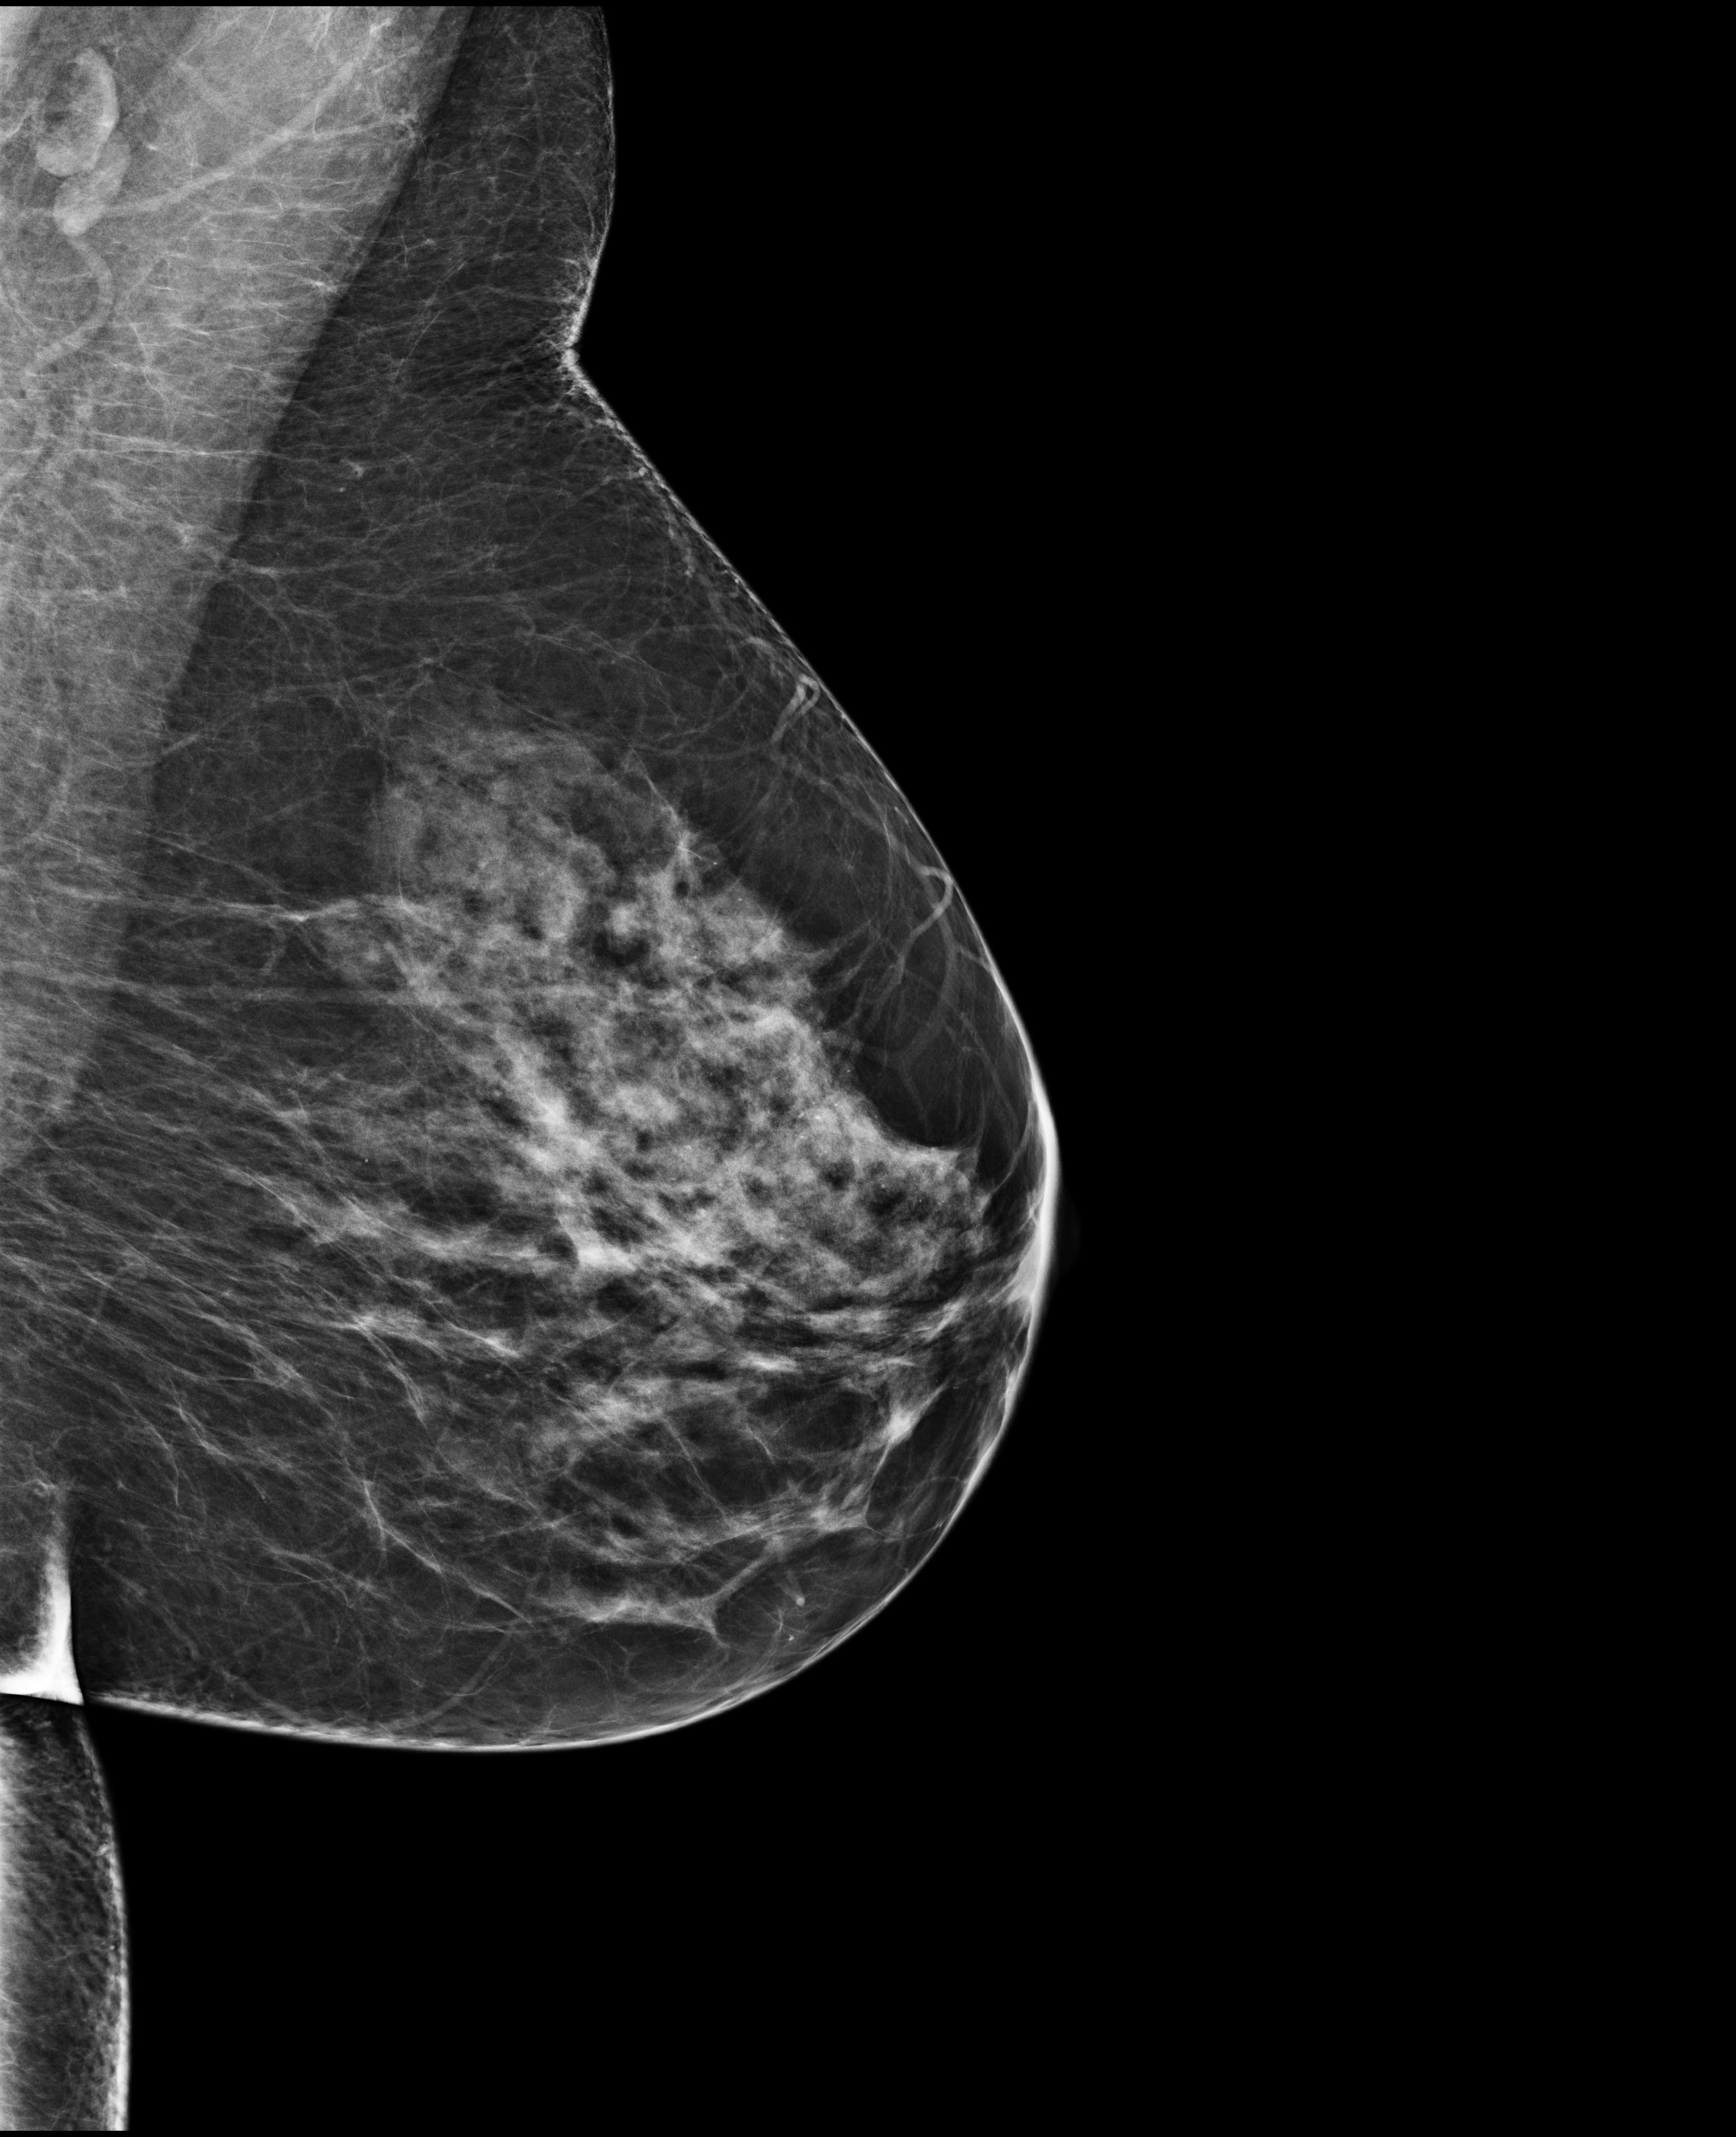
Annual screening mammography examination, compressed breast thickness 68 mm.
Image type: full-field digital mammogram. Breast: left. Projection: MLO view.